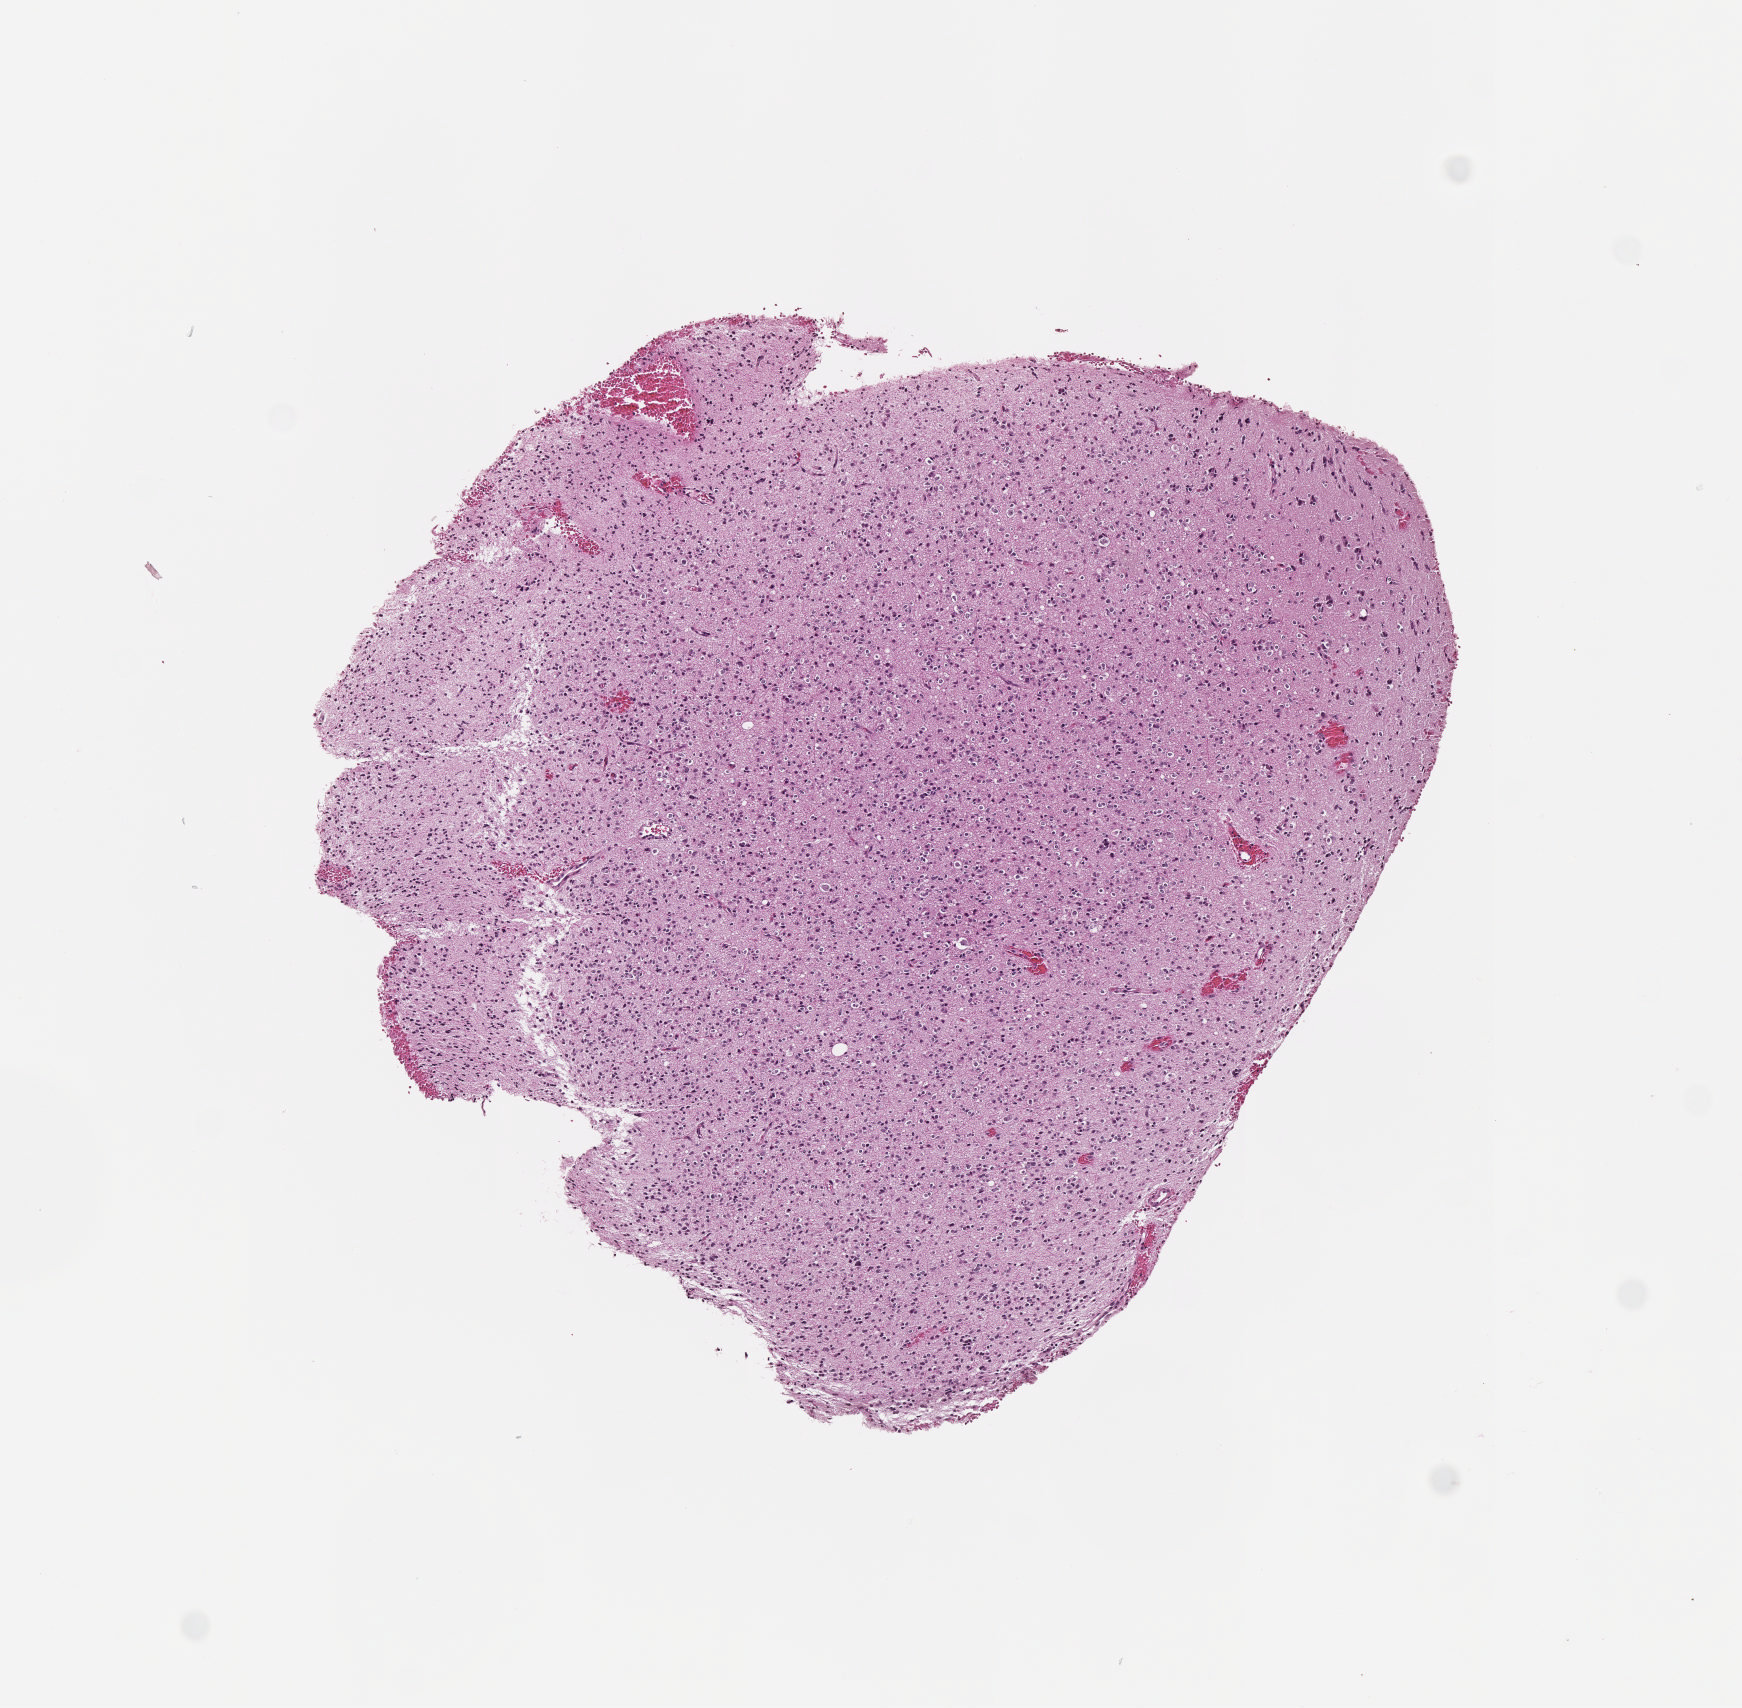
Whole-slide histology image, Hematoxylin and eosin (H&E) stained — a low-resolution overview of the entire scanned area, about 3.5 x 3.5 mm (from a 40x scan), formalin-fixed paraffin-embedded (FFPE) diagnostic section, sample: primary tumour, brain. Male, age 32 years at initial diagnosis. Histologic grade: G2 (moderately differentiated).
Histologic diagnosis: Astrocytoma, NOS (cerebrum).